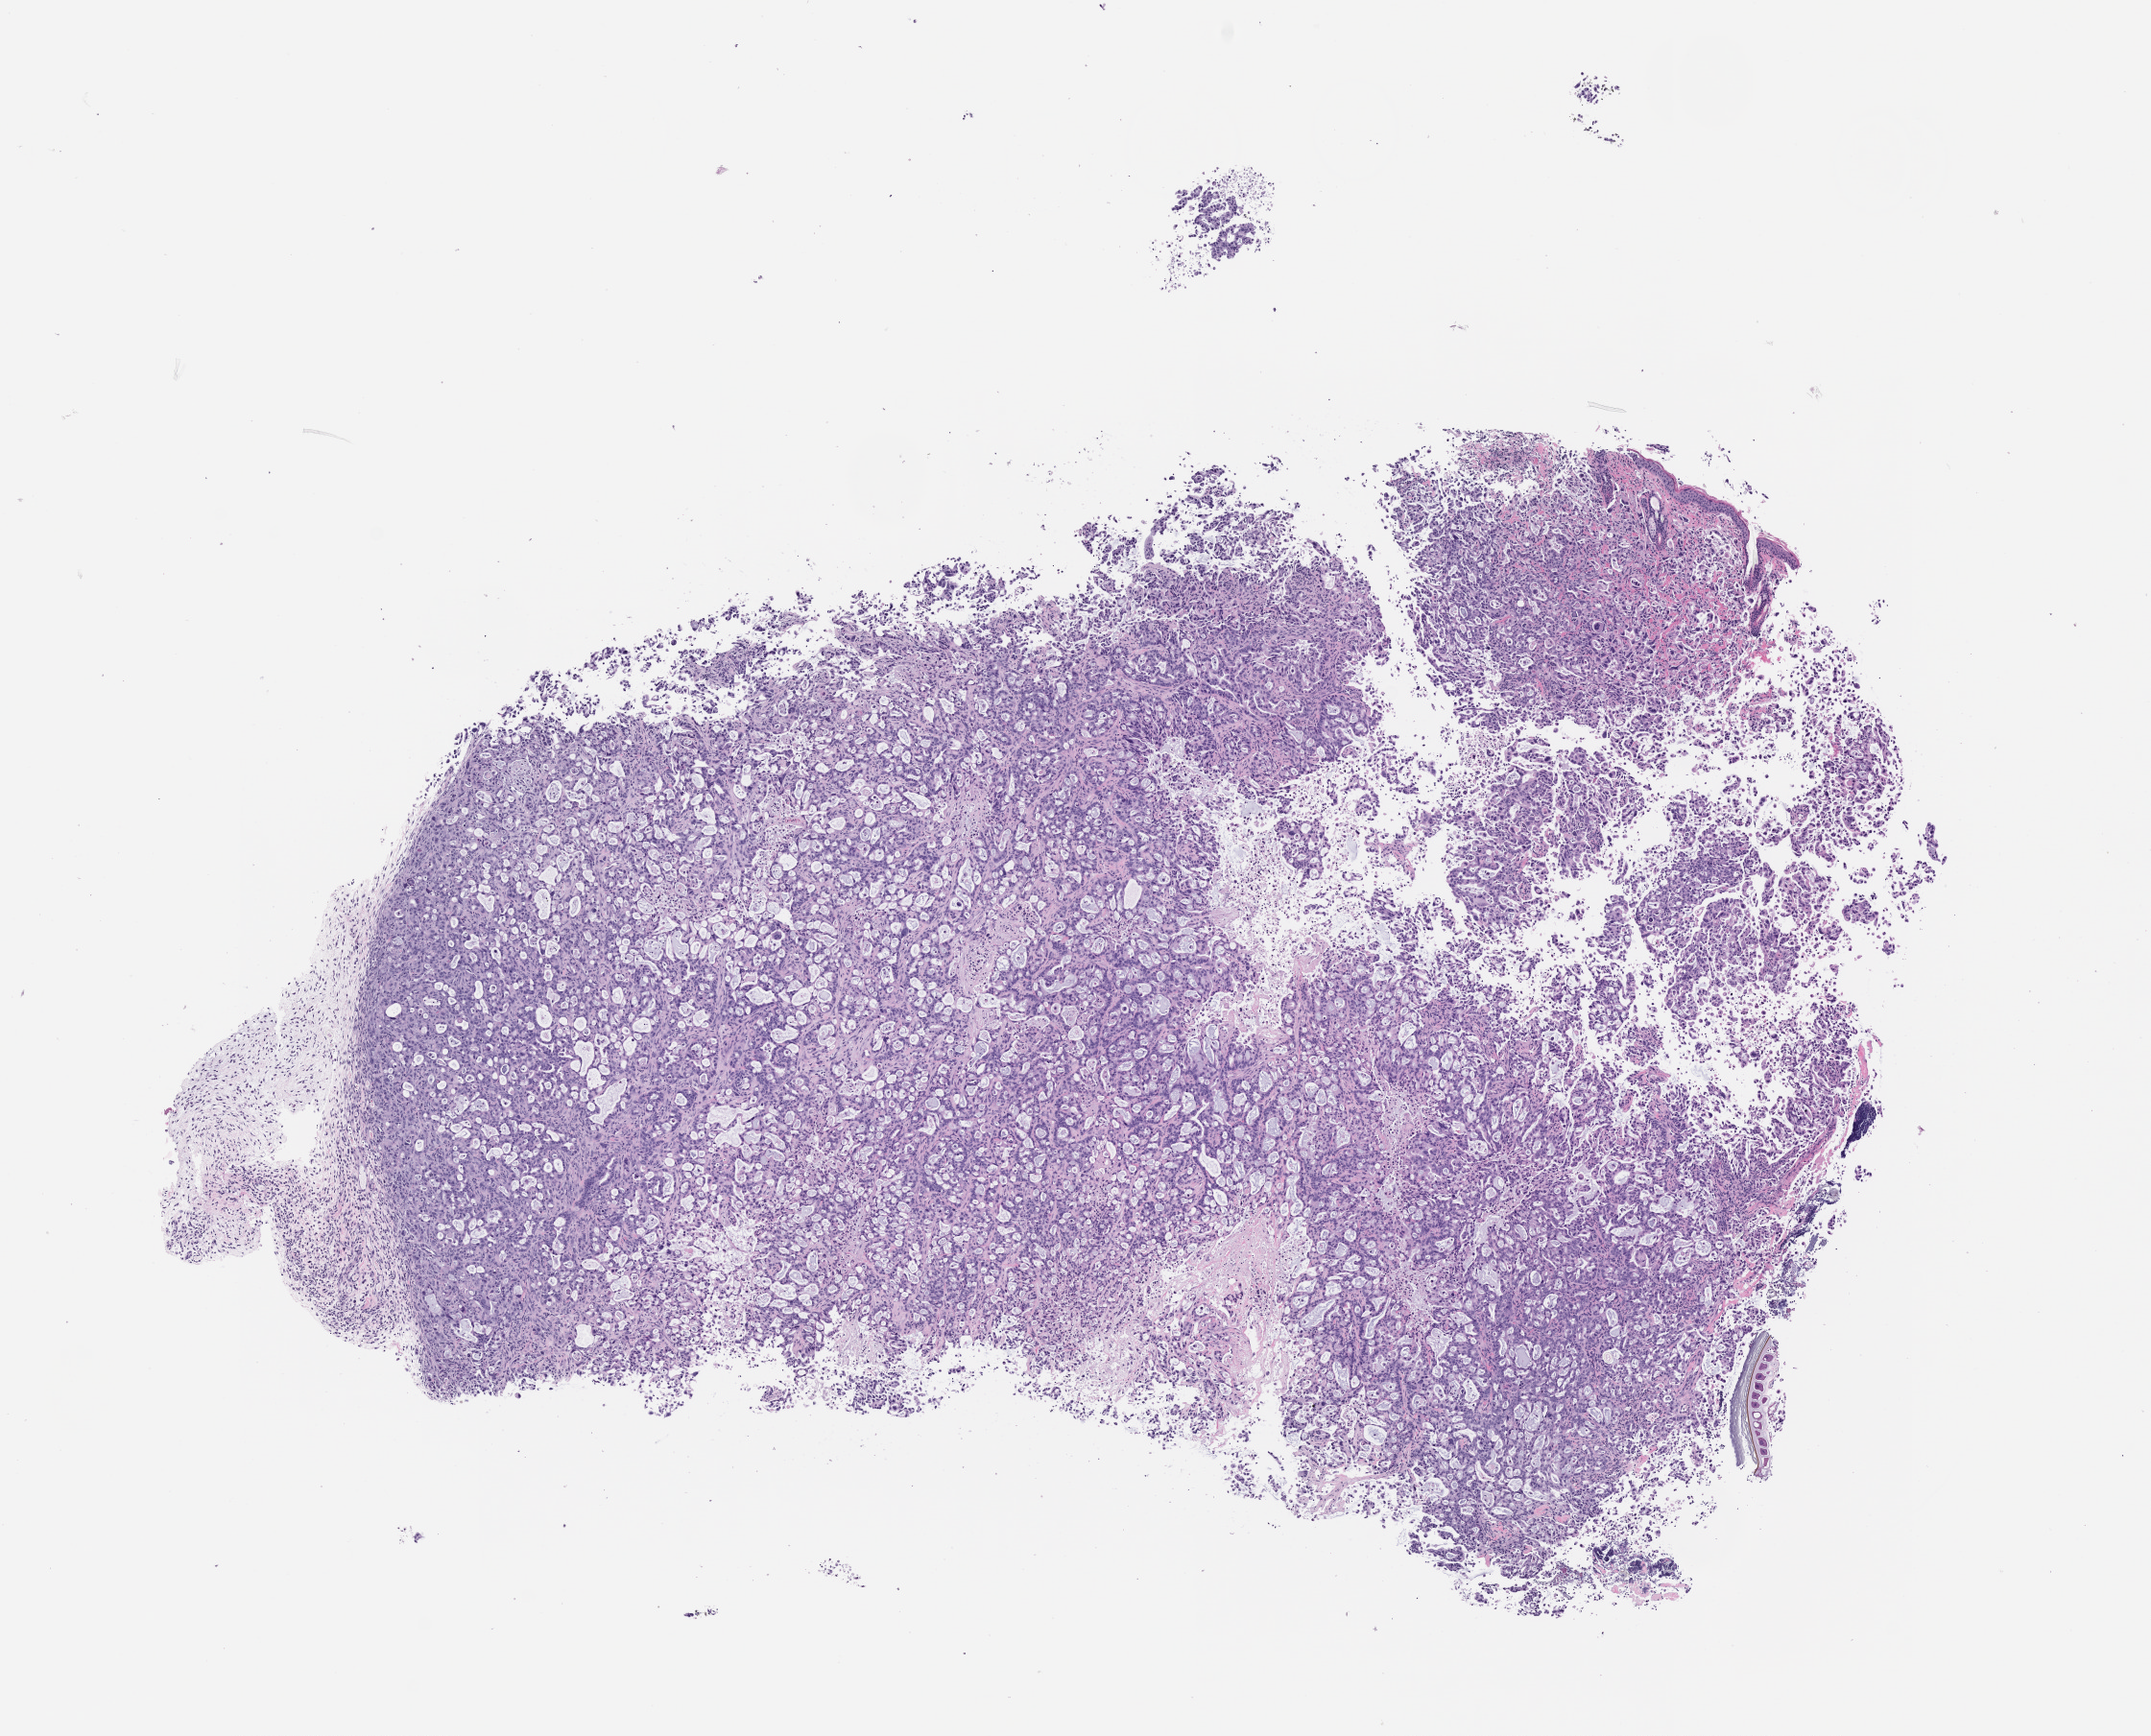
H&E whole-slide image of a patient-derived xenograft (PDX) tumor grown in a mouse, passage 2 — low-resolution overview of the scanned area, about 9.0 x 7.3 mm; formalin-fixed, paraffin-embedded (FFPE) tissue; tumor site category: pancreas.
- originating patient diagnosis: Pancreatic Adenocarcinoma